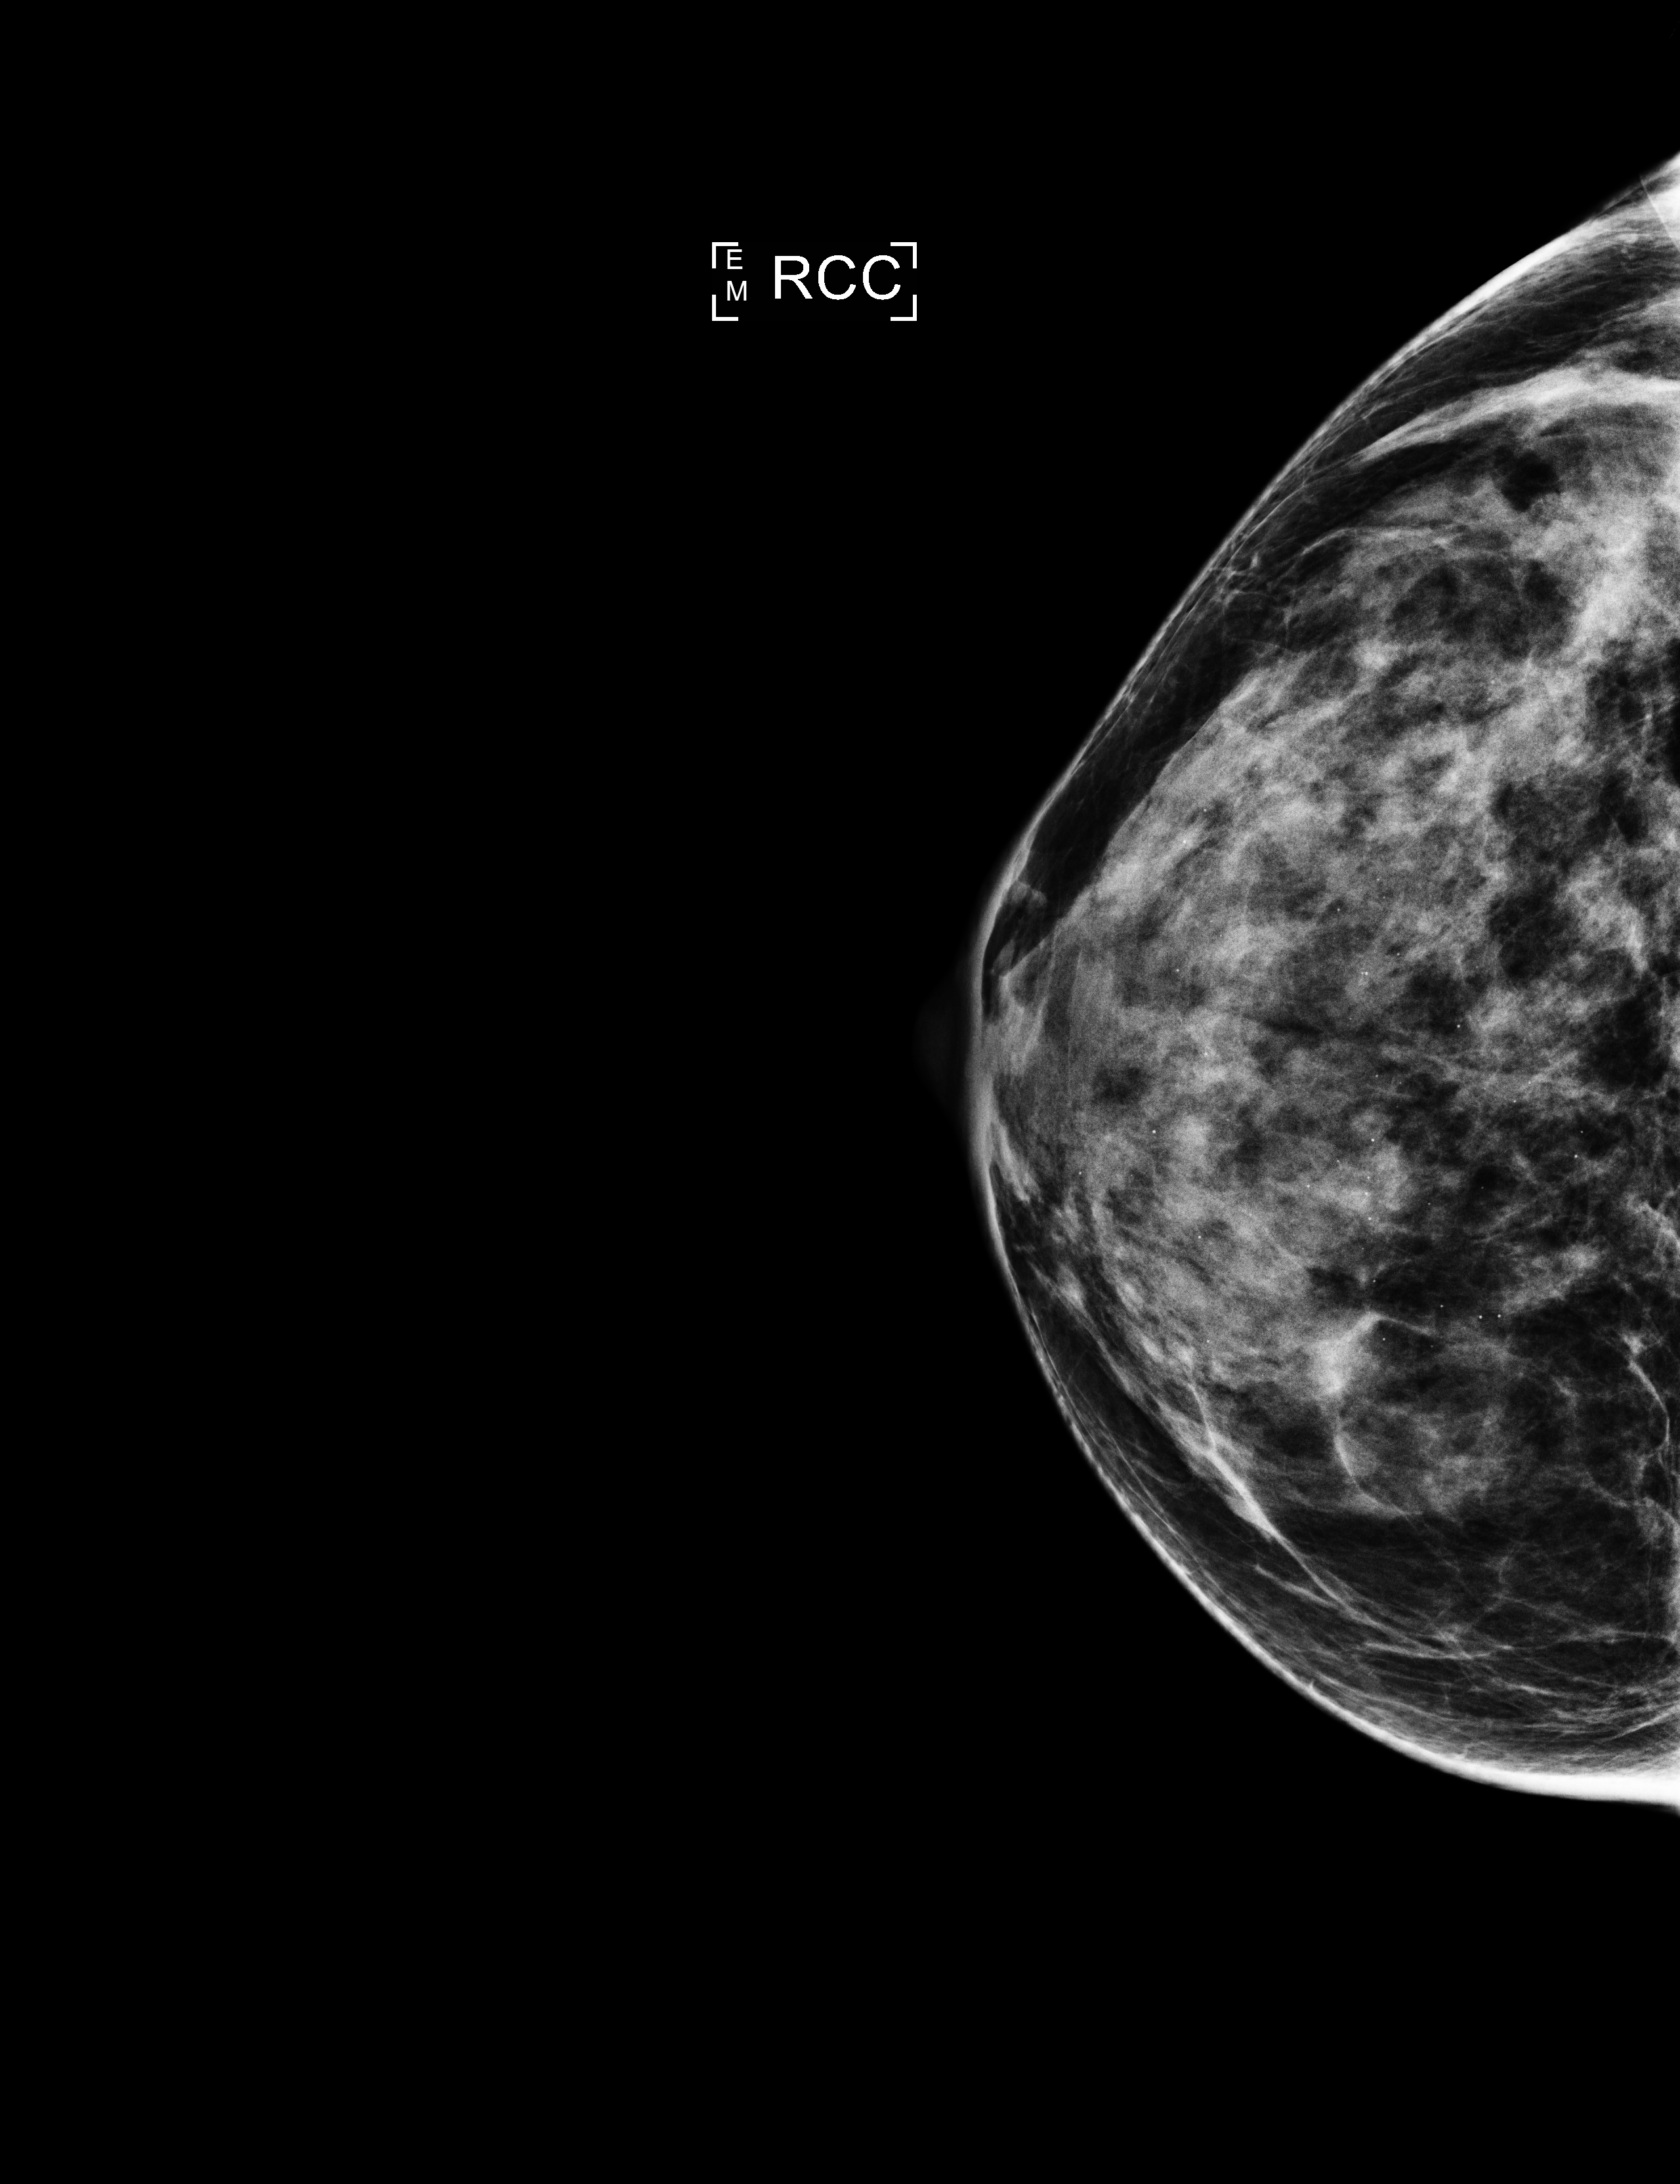
Full-field digital mammogram (FFDM); right breast; craniocaudal (CC) view; annual screening mammography examination; compressed breast thickness 50 mm; system: Selenia Dimensions. Female patient, age 46 years.
- BI-RADS breast density category at the screening exam (both breasts, scale 1–4): 4
- final BI-RADS assessment for this screening round (tomosynthesis exam, both breasts): category 1
- recall: no recall after this screen